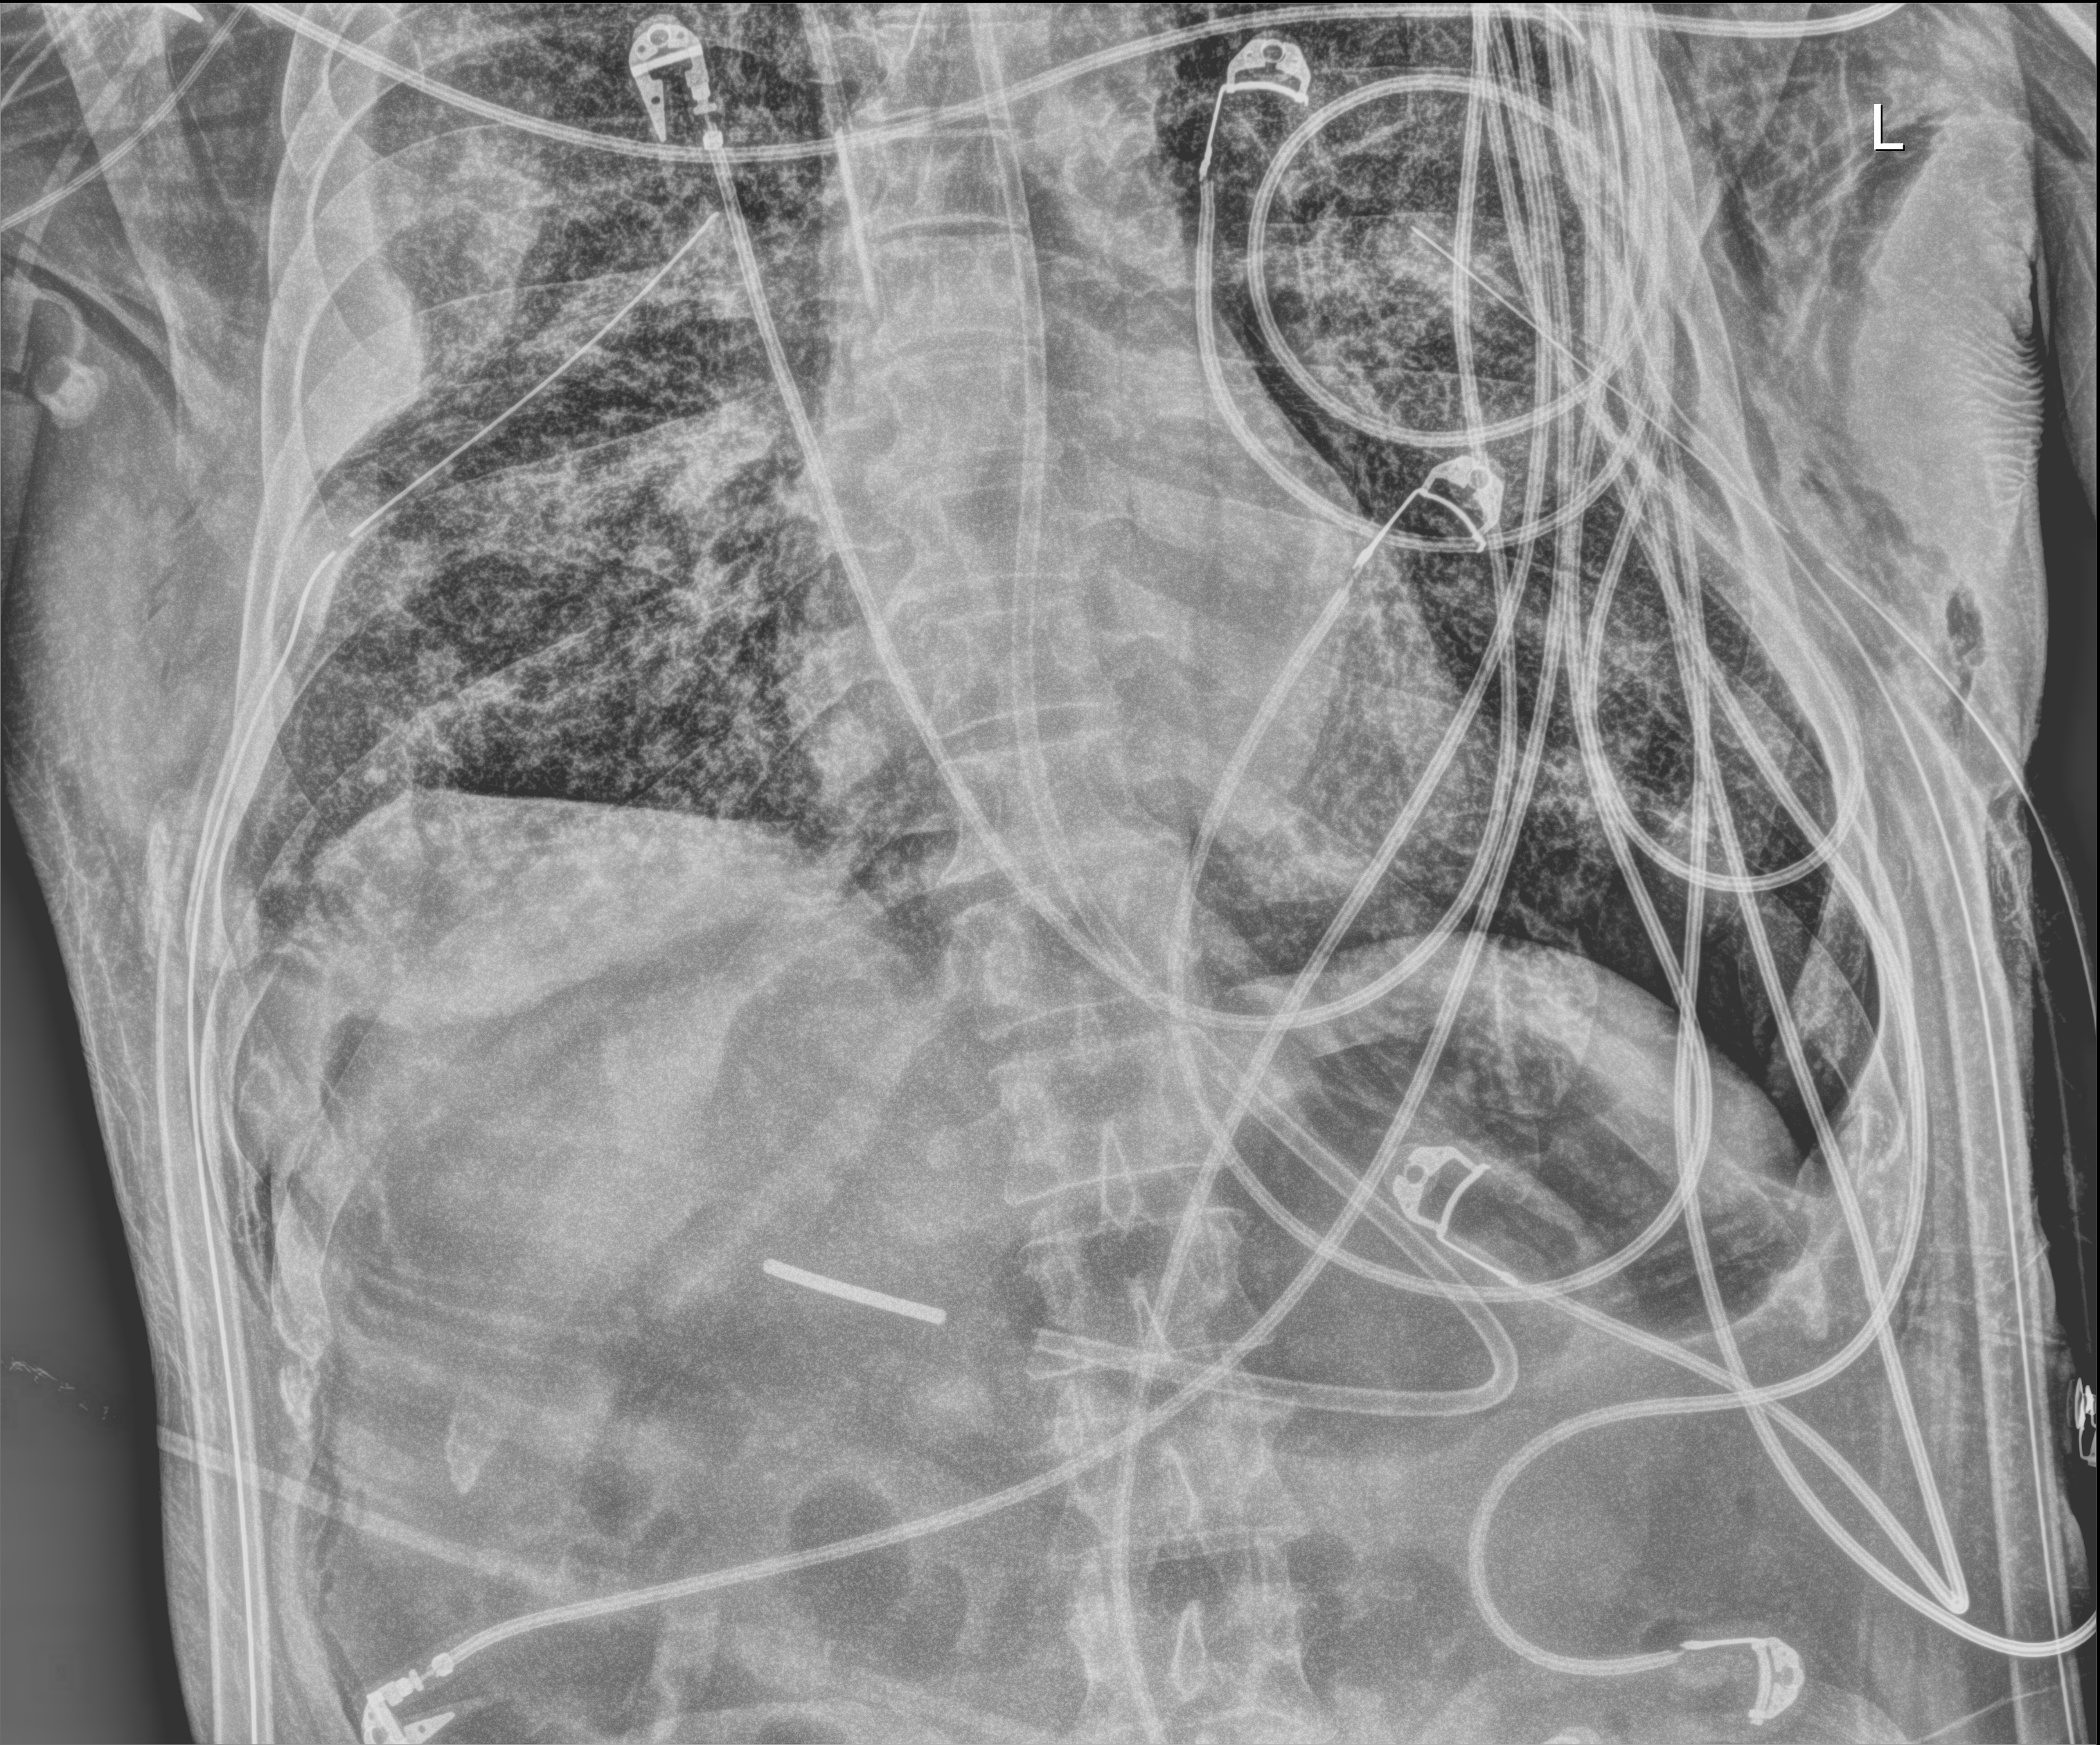
Portable chest radiograph; anteroposterior (AP) projection. Male patient hospitalised with COVID-19, age 18–59 years.
Admission-level facts for this patient (not findings on this image; timing relative to this image not recorded):
- admitted to intensive care during this hospital stay: yes